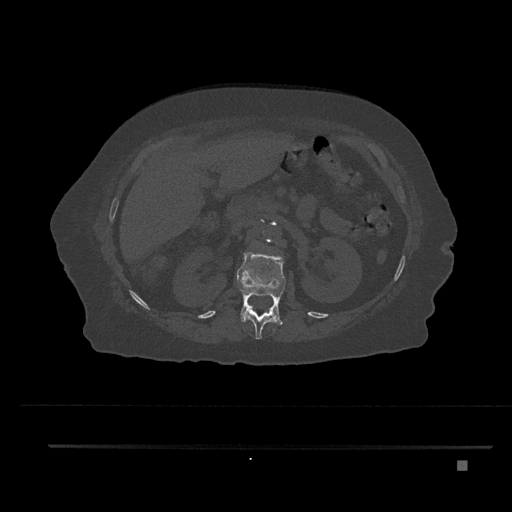
CT including the spine, one axial slice; slice 236 of 797 in the series (ordered by position); 120 kVp; bone window (W 1800 / L 400 HU); 0.5 mm slice thickness; 512 × 512 image matrix, field of view 437 × 437 mm. Female patient, age 76 years. From the clinical record (not read from this slice): primary cancer: lung; vertebrae with lytic lesions (as recorded): T11, L3.
Annotated regions visible in this slice (semi-automatically segmented with operator editing):
- L1 vertebra: bounding box <237,250,286,325> (left, top, right, bottom; pixels)
- T12 vertebra: <245,306,275,340>